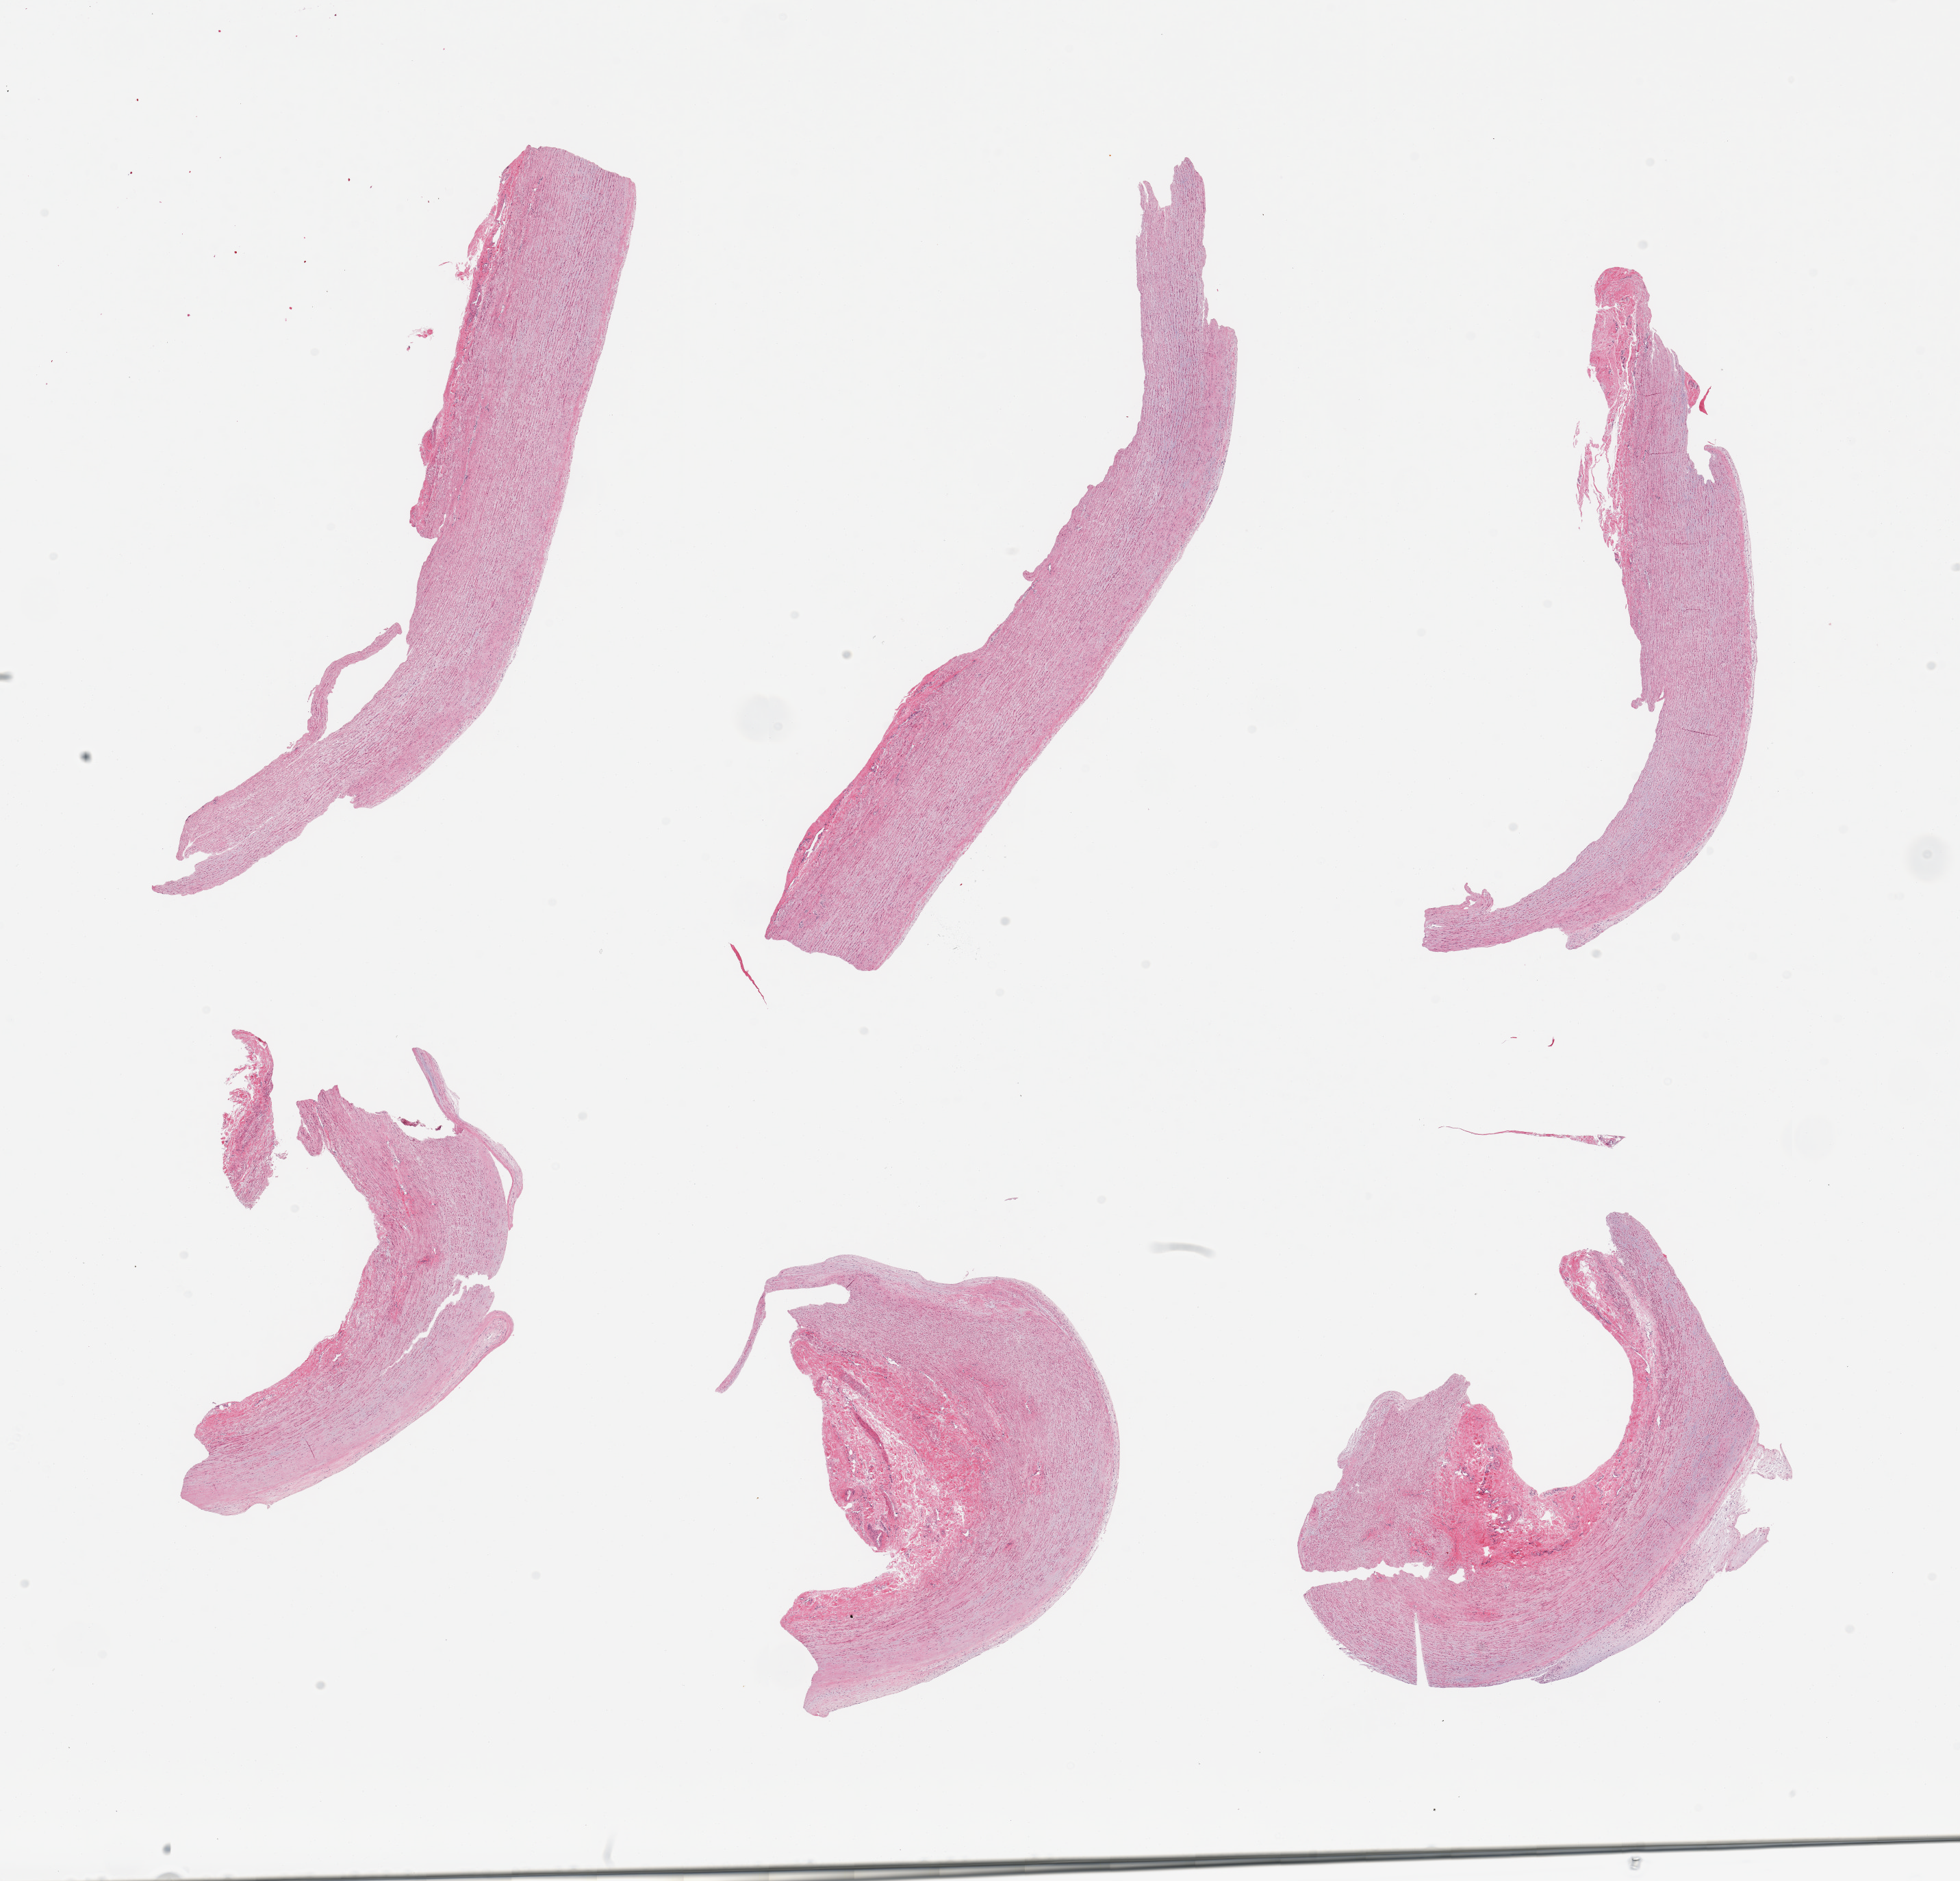
Whole-slide image, H&E stain, brightfield, low-resolution overview of the scanned area, about 22.6 x 21.7 mm; PAXgene-fixed paraffin-embedded (PFPE) section; section of aorta (target tissue); tissue donor sample. Female donor.
- review note (as recorded): 6 pieces; flat plaques